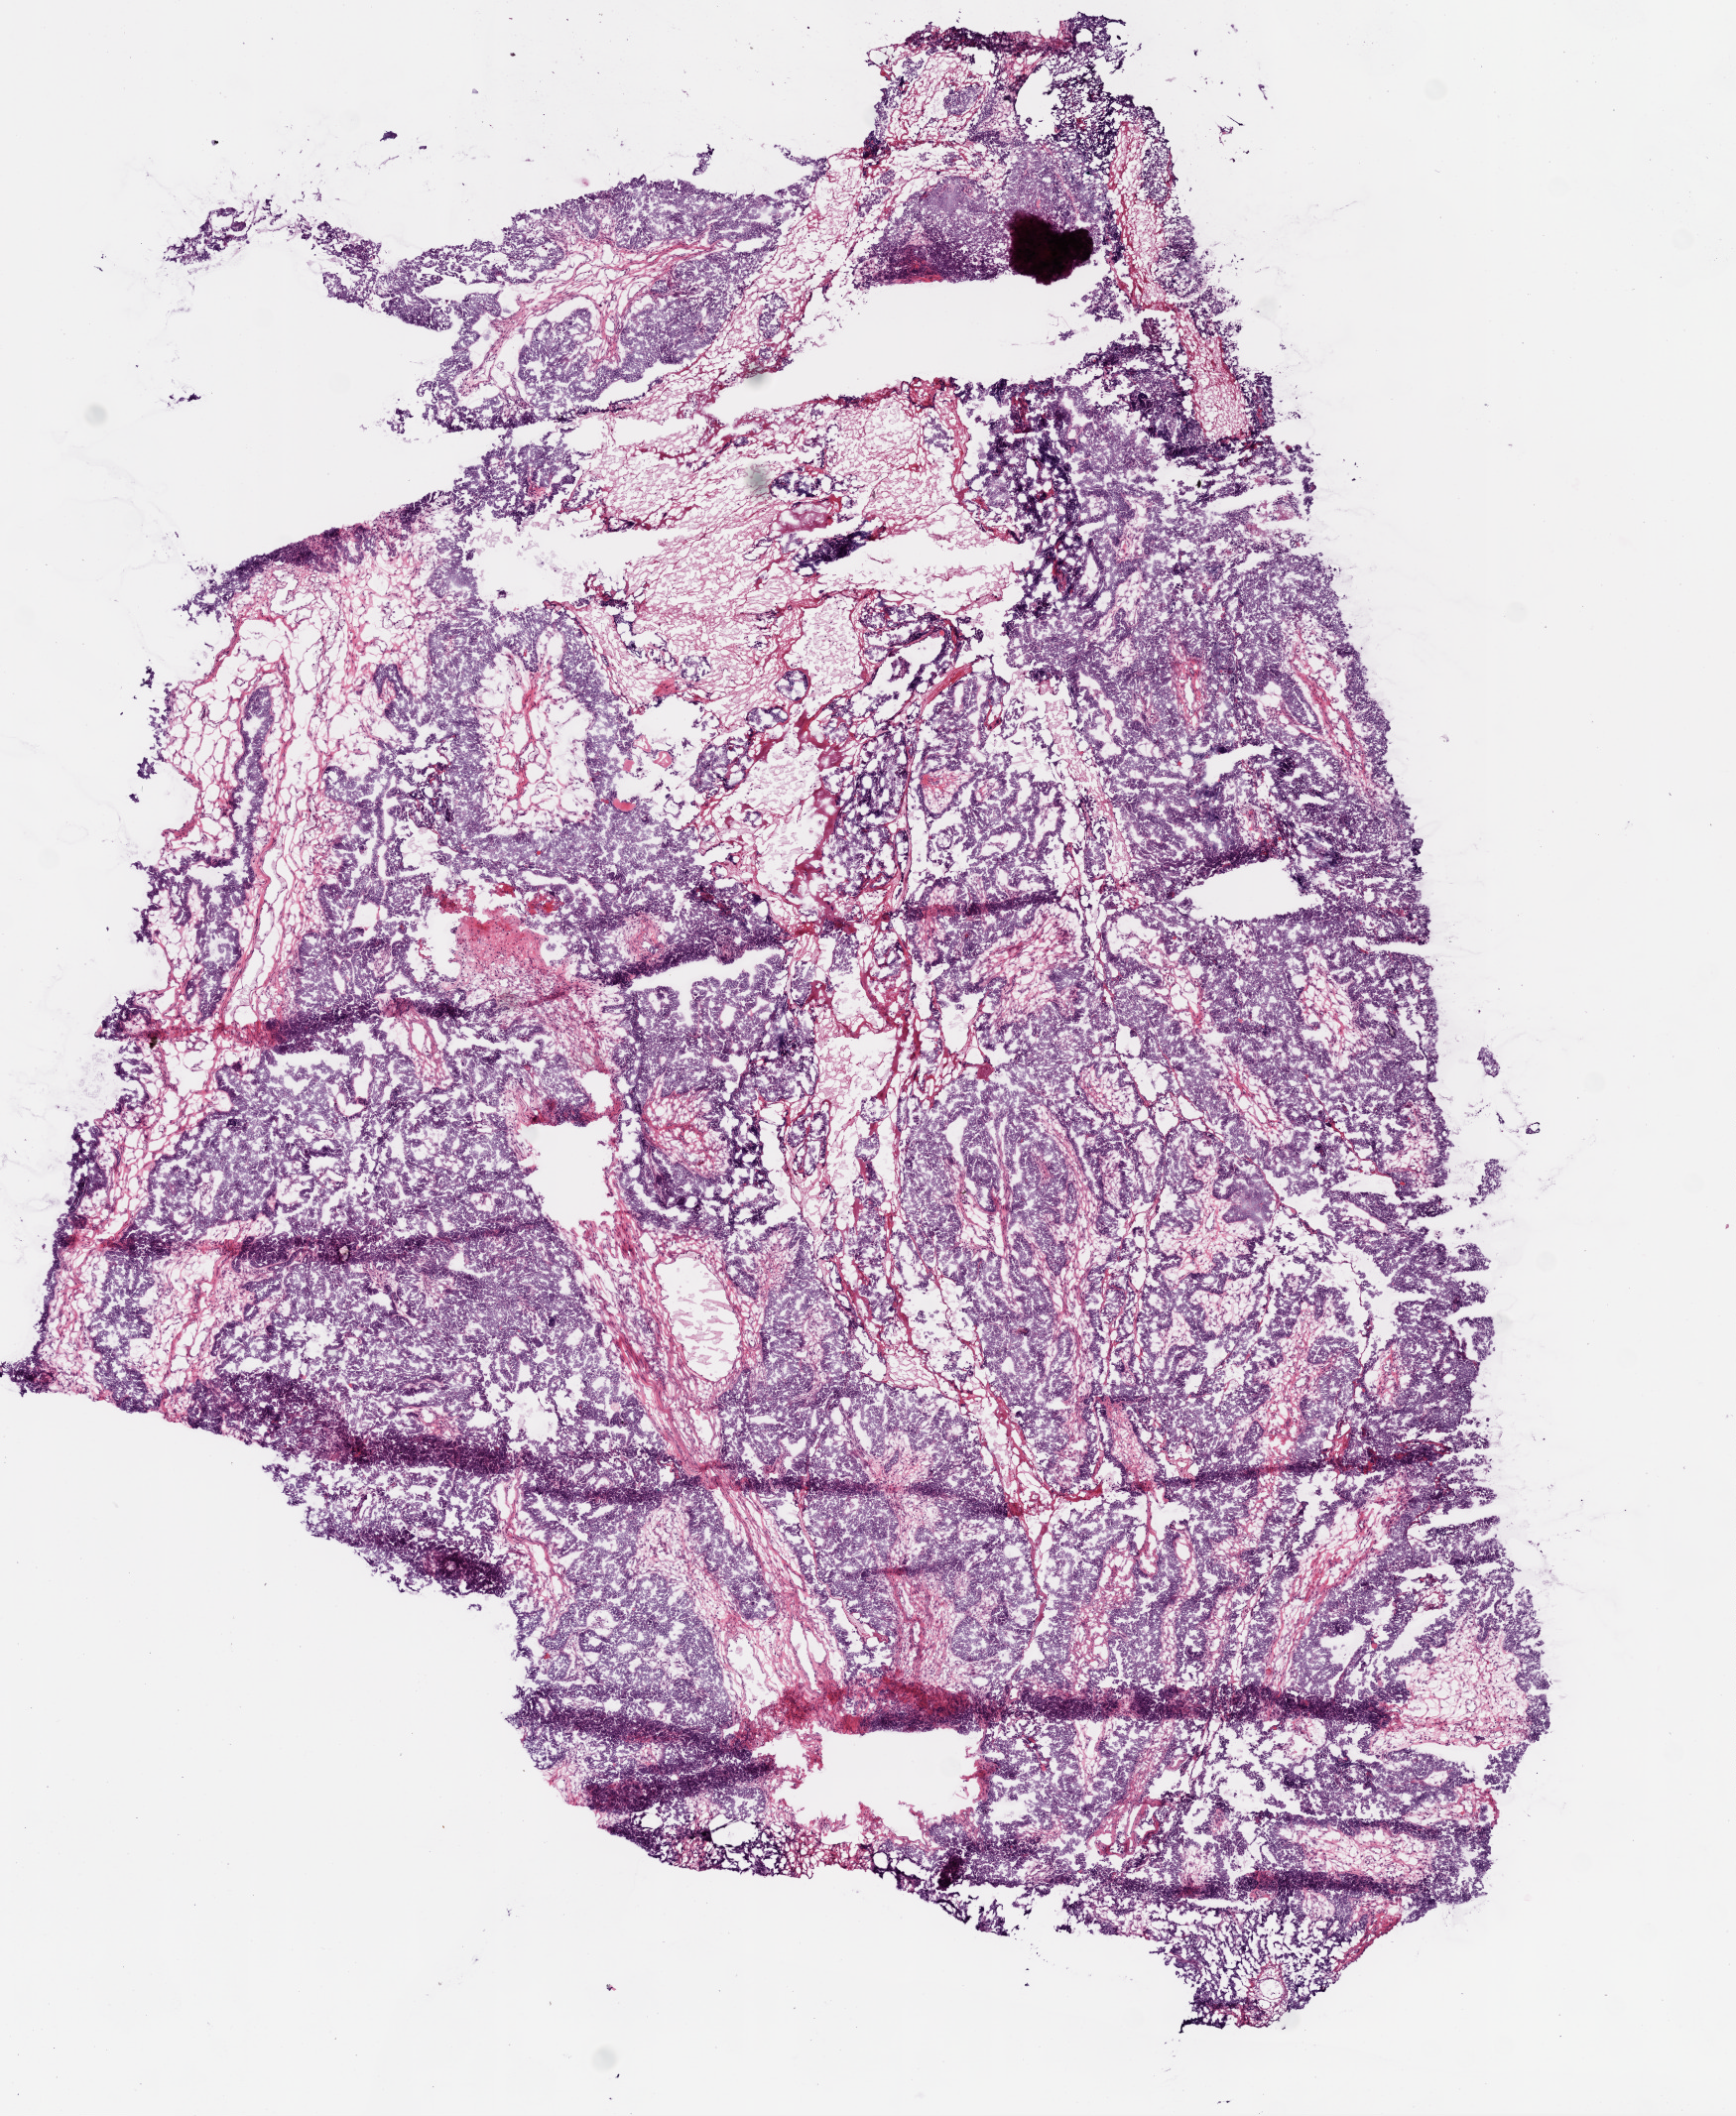
Whole-slide histology image, Hematoxylin and eosin (H&E) stained, a low-resolution overview of the entire scanned area, about 7.0 x 8.6 mm (slide scanned at 20x). Frozen section from the bottom of the tissue portion. Primary tumour sample from the ovary. Female patient; age at initial diagnosis 45 years.
Diagnosis: Serous cystadenocarcinoma, NOS.